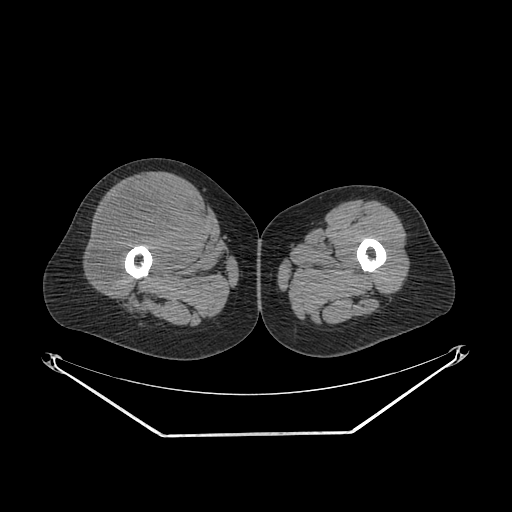
CT of an extremity soft-tissue mass (from a PET/CT study), one axial slice. Position 249 of 311 along the scan axis. 140 kVp. Soft-tissue window (W 400 / L 40 HU). 512 × 512 image matrix, field of view 500 × 500 mm. Female patient. From the clinical record (not read from this slice): histological type: pleiomorphic undifferentiated sarcoma; grade: high; site of the primary tumour: right quadricep.
Structures marked on this image (expert contour drawn on MRI and transferred to this co-registered scan by the dataset authors):
- tumour plus oedema (research contour): bounding box (x1, y1, x2, y2) in pixels: (94, 185, 197, 287)
- tumour (research contour): (94, 185, 197, 287)